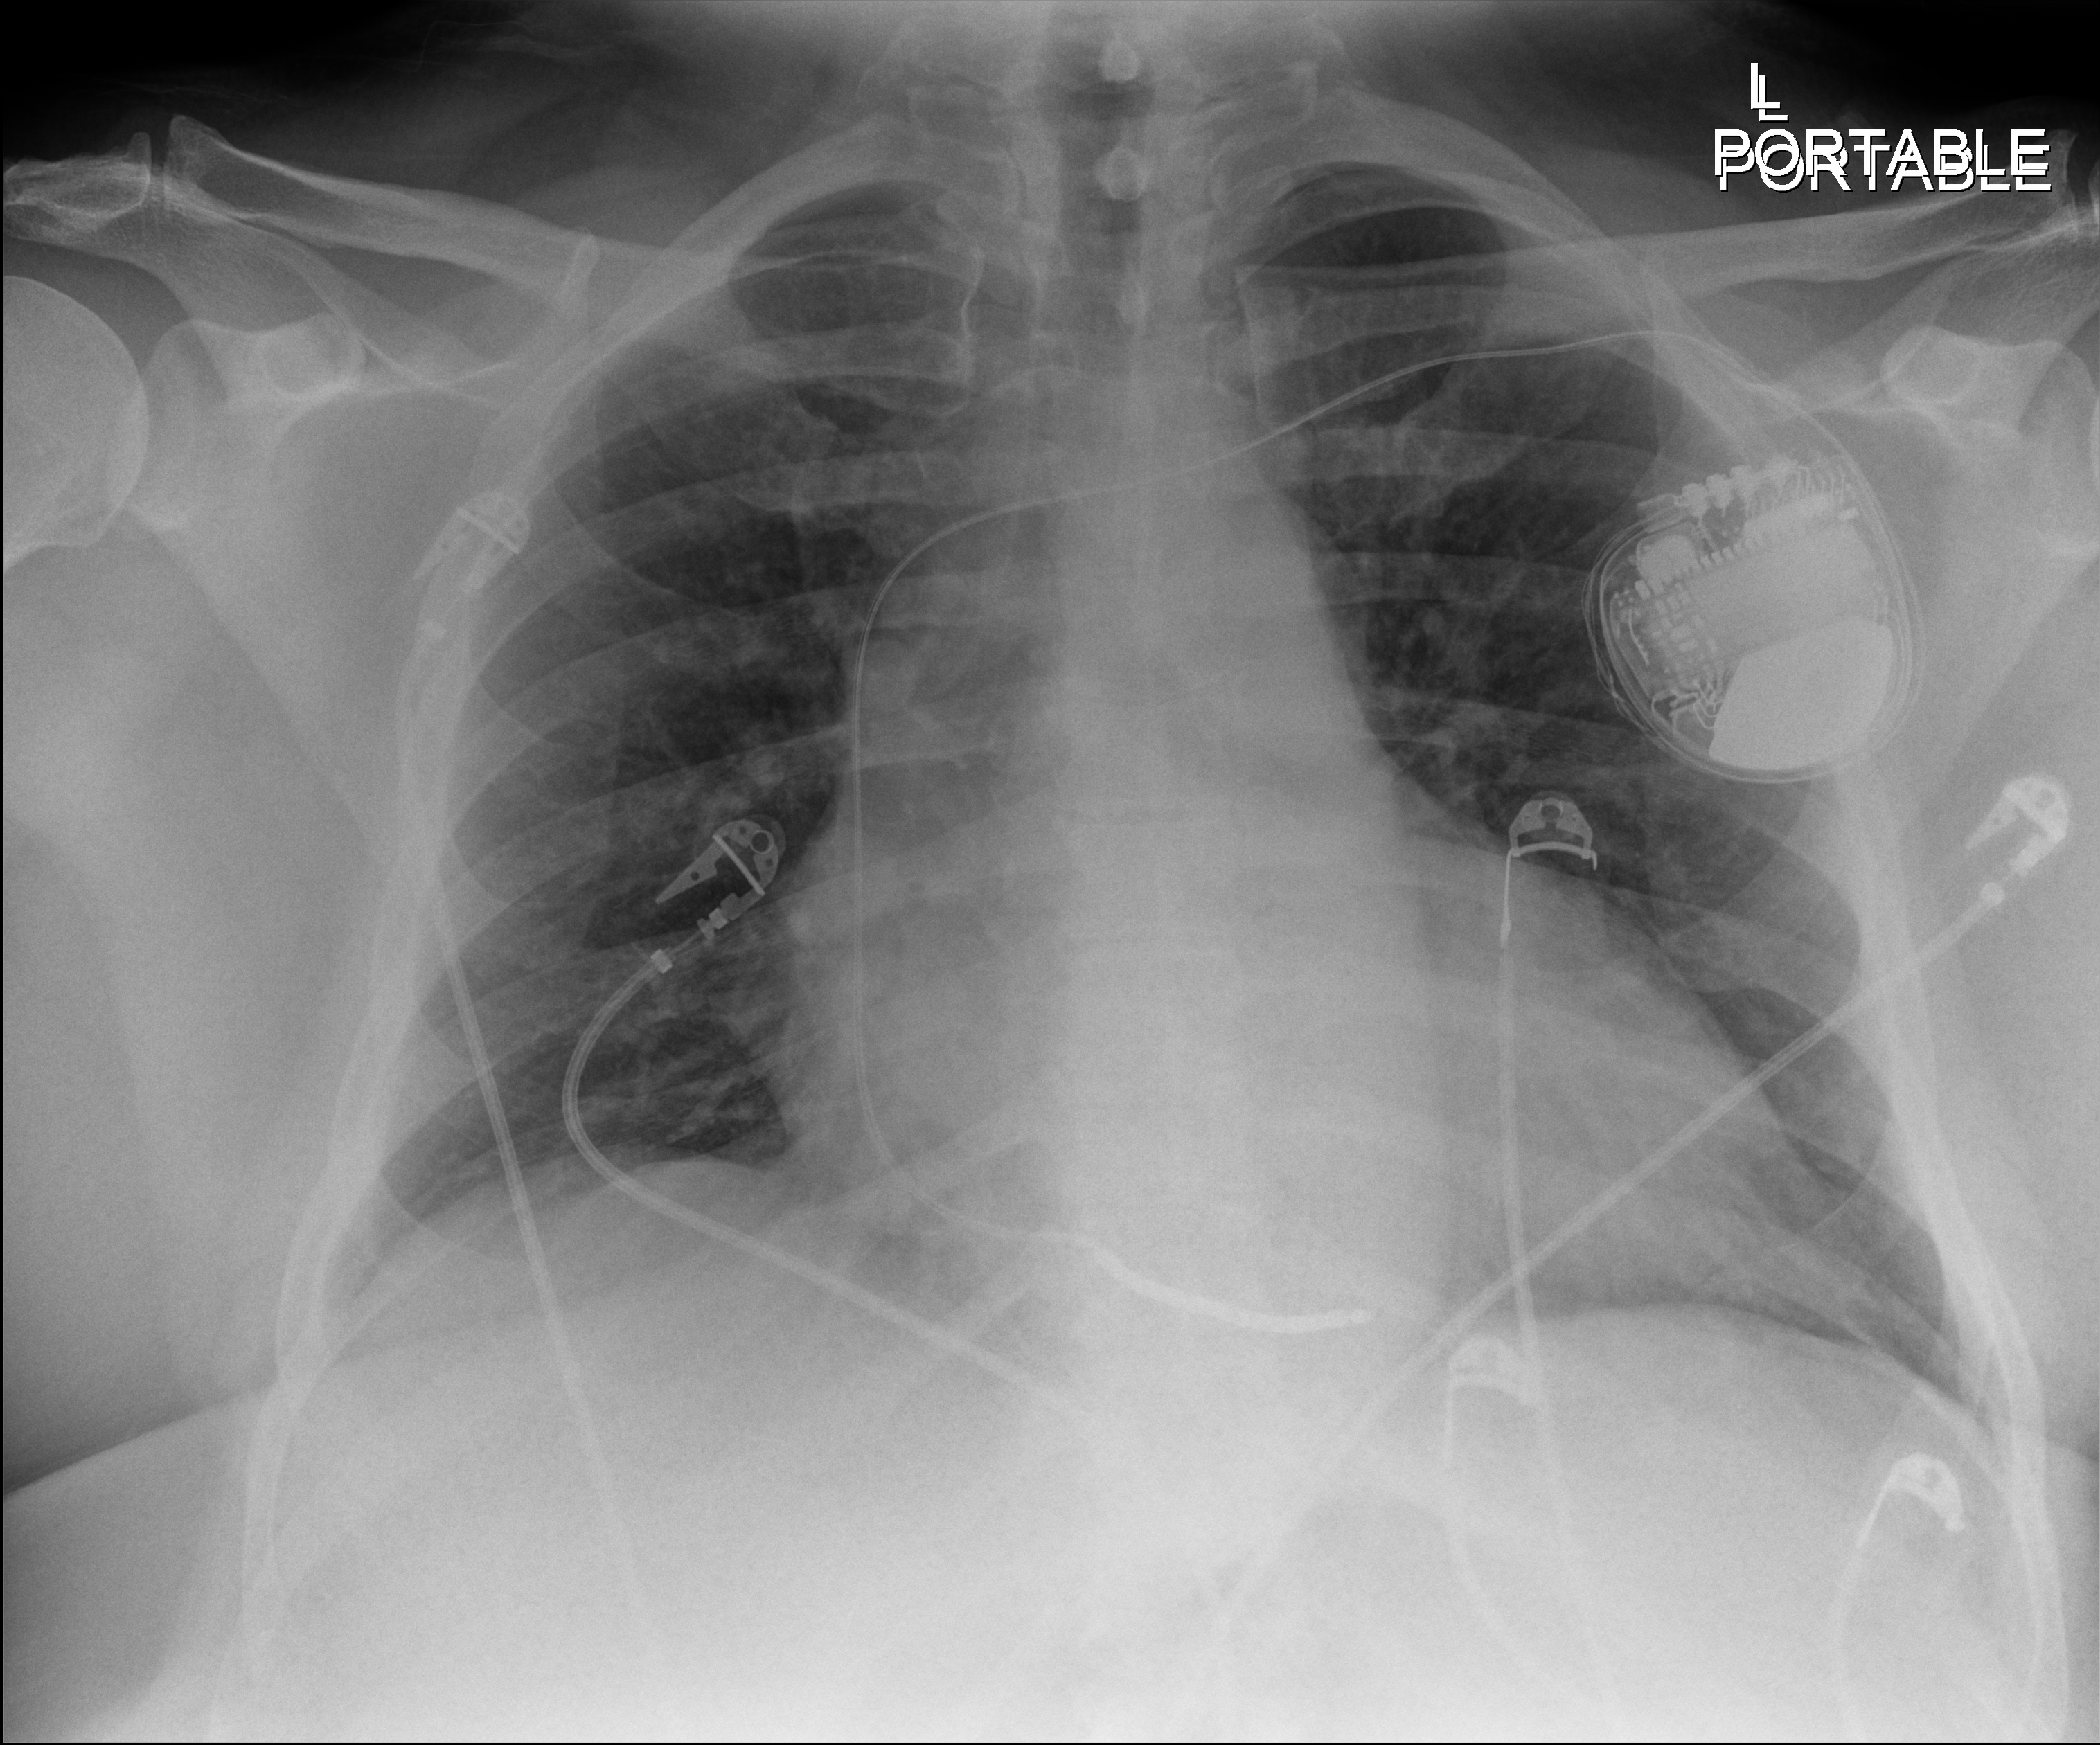
Chest radiograph (digital radiography). Male patient hospitalised with COVID-19, age 18–59 years.
From the hospital-stay record, not from the radiograph (when in the stay this image was taken is not recorded):
- other chronic lung disease (admission record): yes
- mechanically ventilated during this hospital stay: no